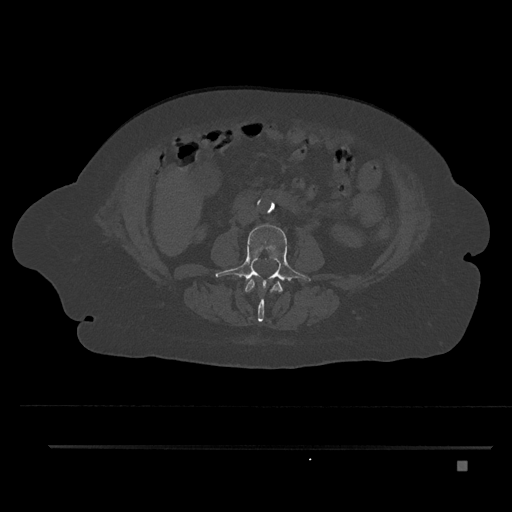
CT including the spine, one axial slice; slice 135 of 797 in the series (ordered by position); reconstruction kernel Br40s/3; bone window (W 1800 / L 400 HU); 512 × 512 image matrix, field of view 437 × 437 mm. Patient: female, 76 years. Case-level facts recorded for this patient, not image findings: primary cancer: lung.
Annotated regions visible in this slice (semi-automatic segmentation, software-assisted and operator-edited):
- L2 vertebra: bounding box <245,279,283,322> (left, top, right, bottom; pixels)
- L3 vertebra: <215,224,311,290>